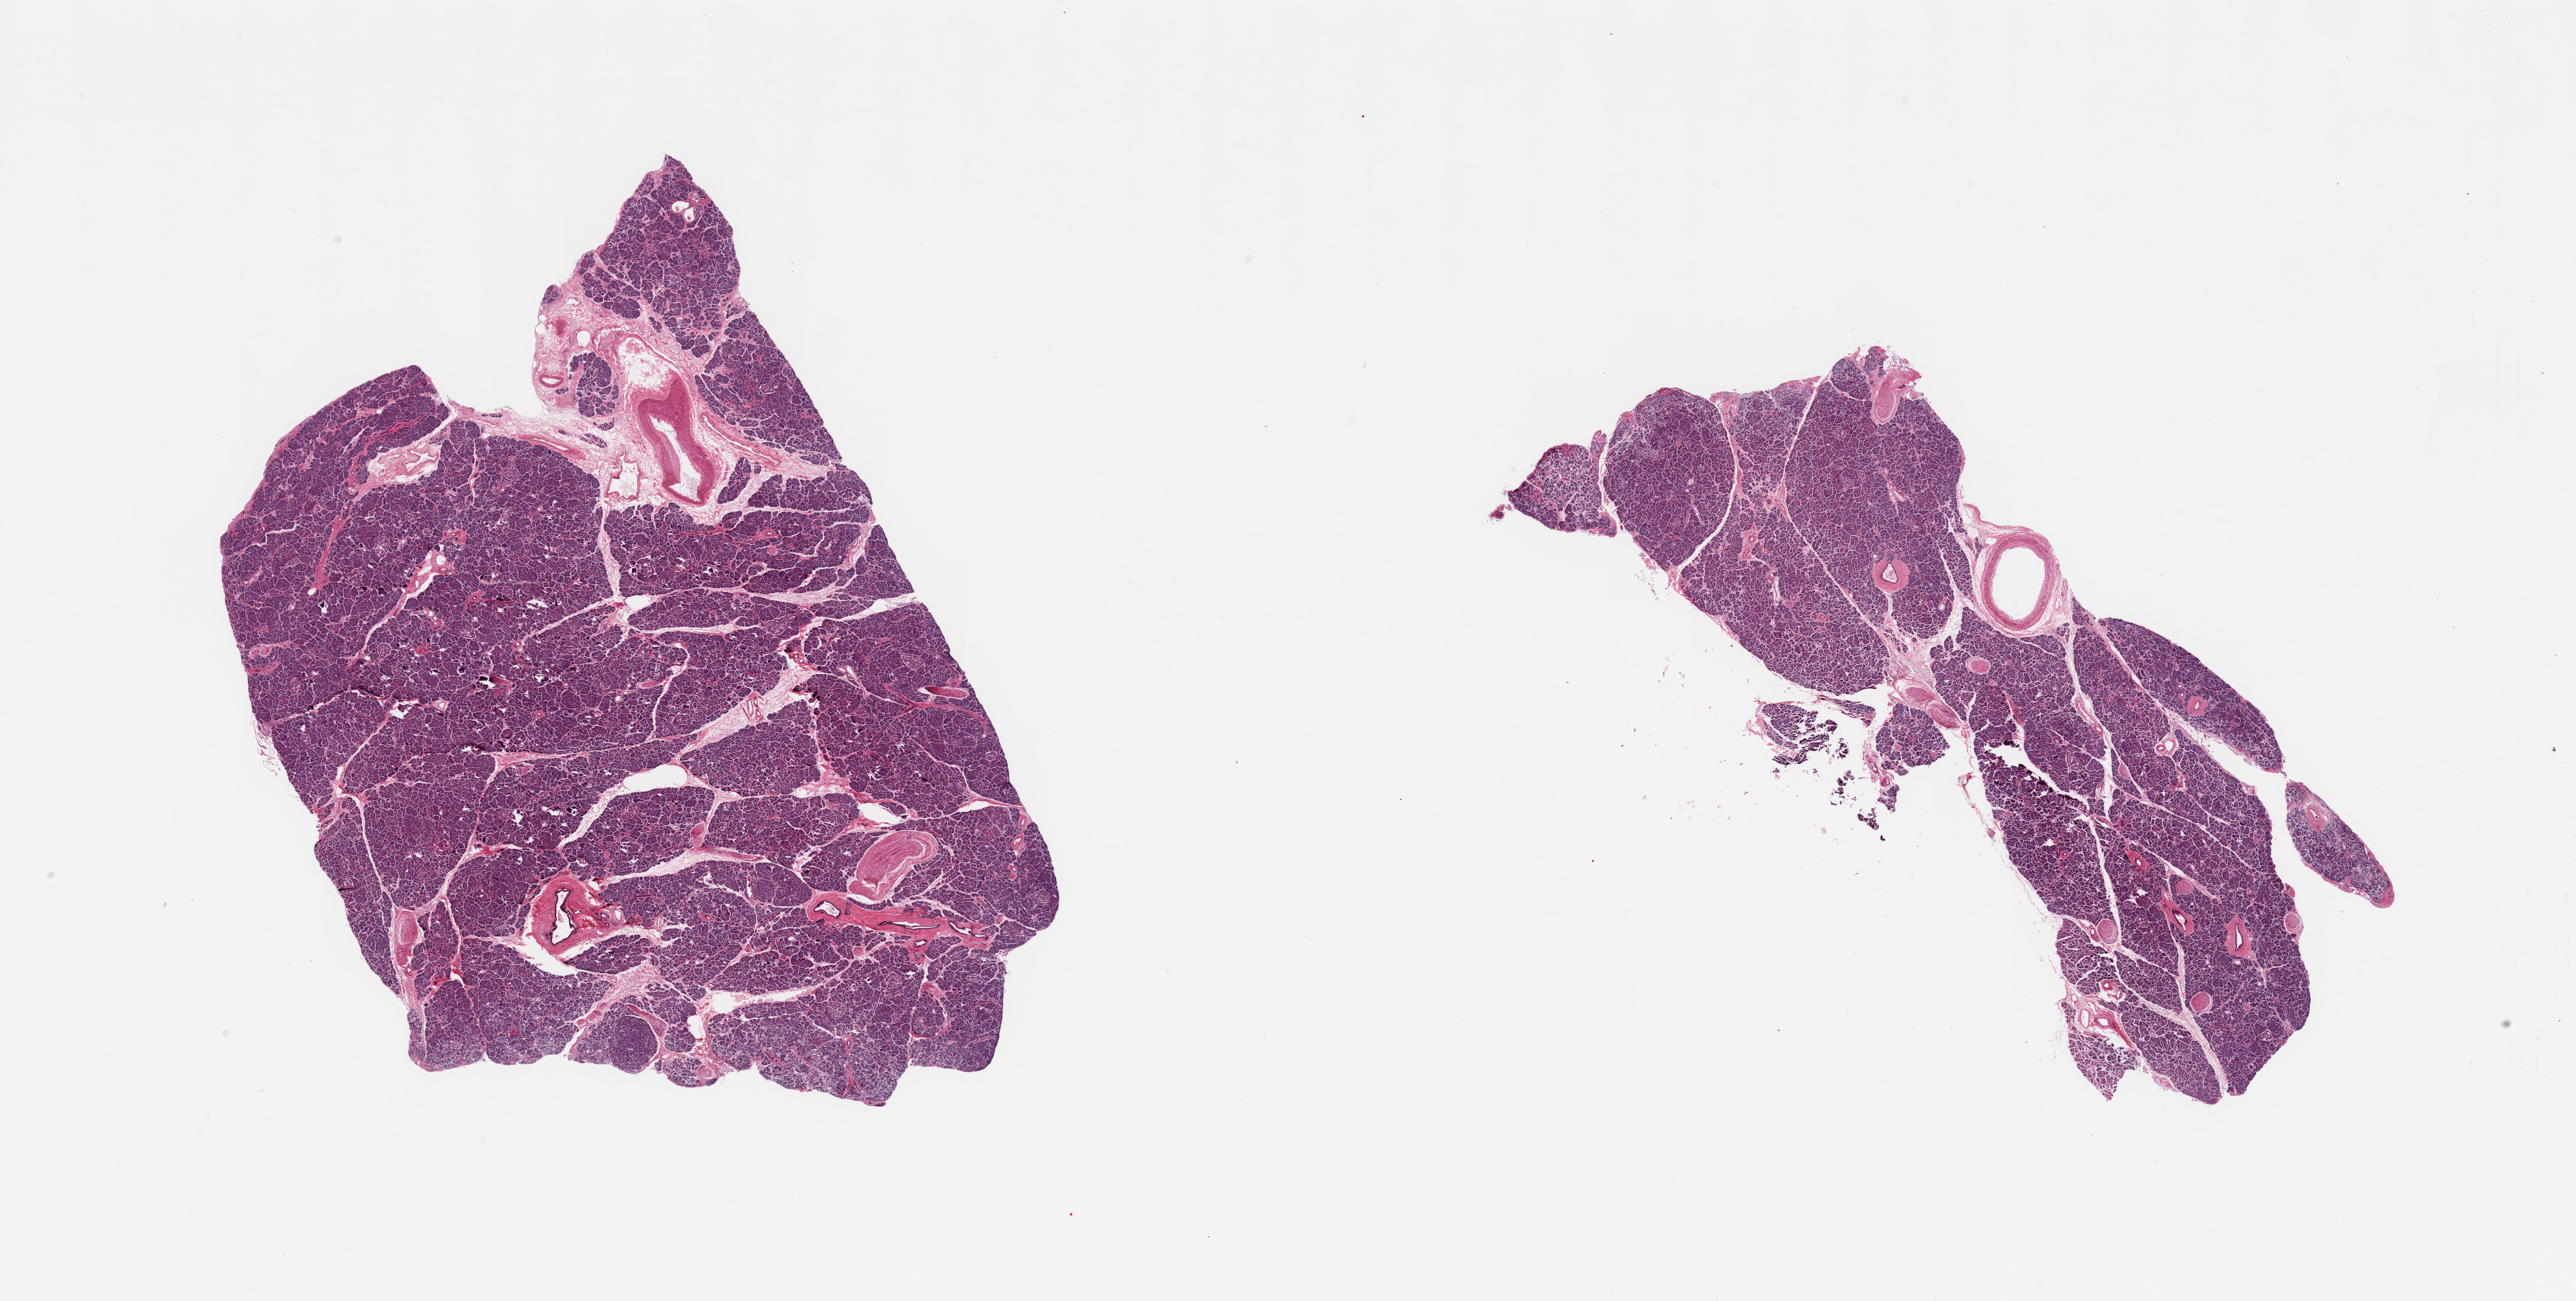
Haematoxylin and eosin whole-slide image — a low-resolution overview of the entire scanned area, about 31.5 x 15.9 mm; PAXgene-fixed, paraffin-embedded tissue; target tissue: pancreas; tissue donor sample. Donor sex: male.
Reviewer comment on this tissue sample: 2 pieces; well preserved parenchyma and Langerhans islets; moderately autolyzed septal fat prominent vessels and nerves.